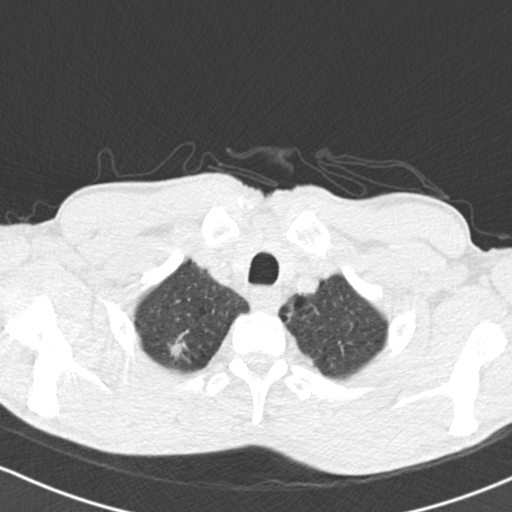
Axial slice from a low-dose chest CT screening exam, baseline screening round, lung window (W 1500 / L -600 HU), 2 mm slice thickness, standard (soft-tissue) reconstruction kernel (B30f), slice 25 of 151 in the series. Male participant, aged 64 years at enrolment. Current smoker at enrolment.
Lesion marked by an expert reader, bounding box <148,325,201,379> (left, top, right, bottom; pixels). The exam's reader record, not a measurement of the box and not confirmed to be the same lesion: non-calcified nodule or mass ≥4 mm, right upper lobe, 13 × 11 mm, spiculated (stellate) margins, soft tissue attenuation. Official screen result: positive, change unspecified: nodule(s) >= 4 mm or enlarging nodule(s), mass(es), or other non-specific abnormalities suspicious for lung cancer. Participant outcome: lung cancer diagnosed 161 days after this screen — adenocarcinoma, NOS, right upper lobe, poorly differentiated (G3), stage IA (AJCC 6th edition), 13 mm at pathology.